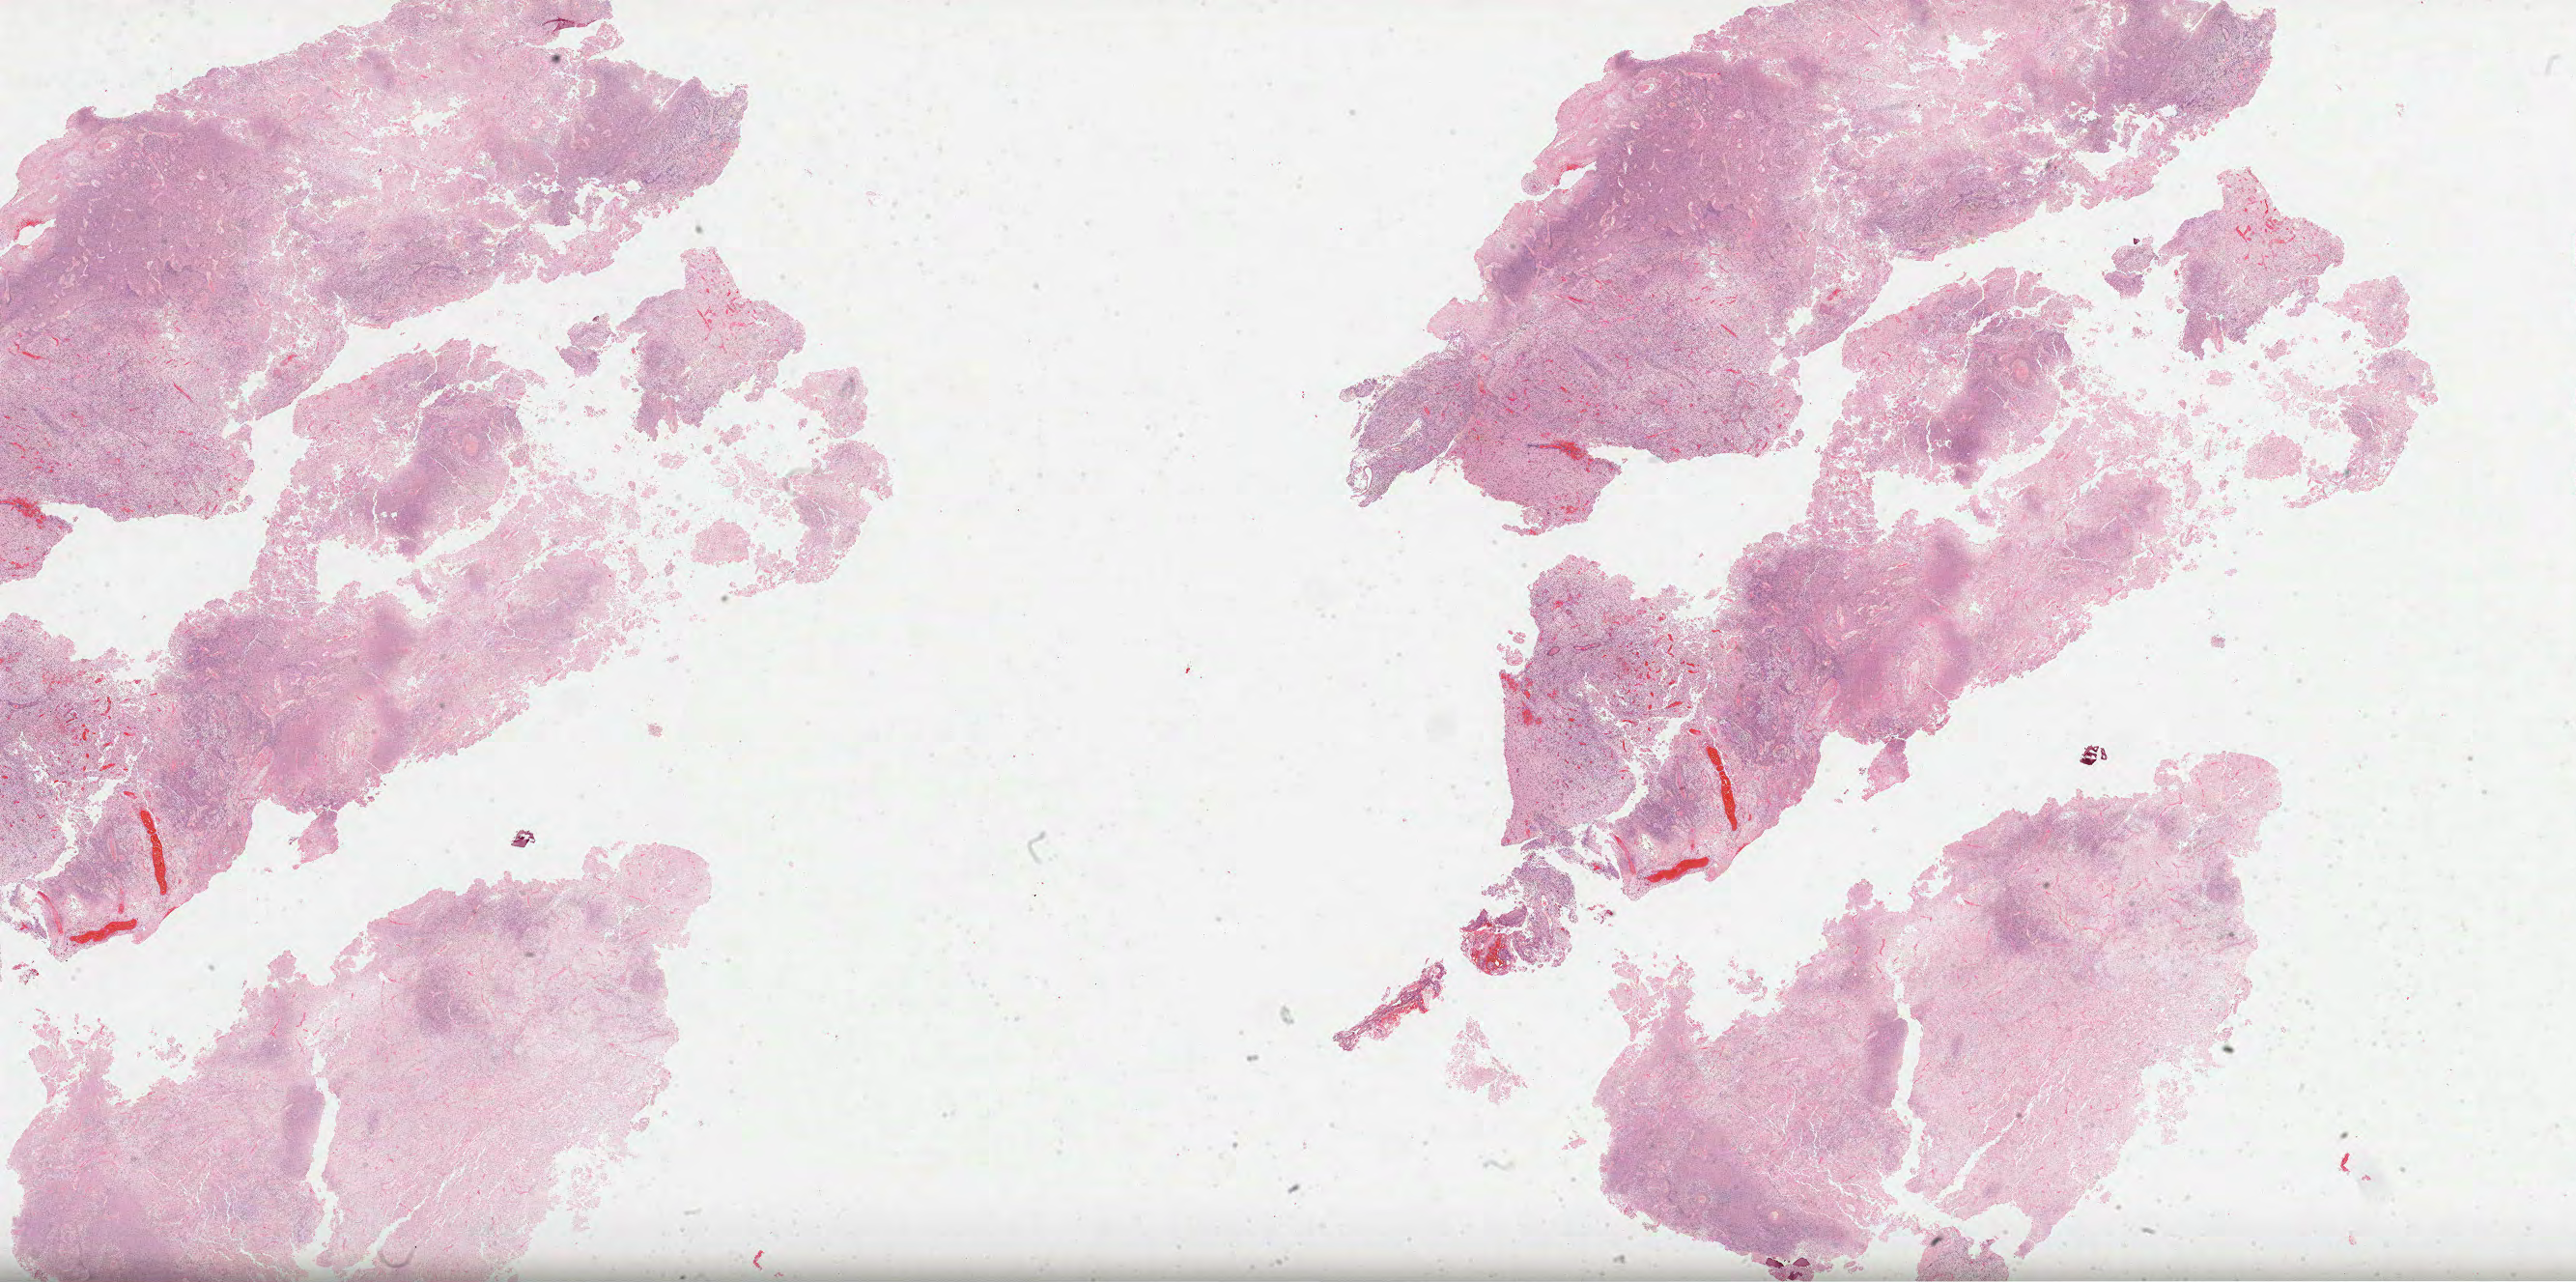
Whole-slide histology image, H&E, a low-resolution overview of the entire scanned area, about 43.0 x 21.4 mm (slide scanned at 40x); formalin-fixed paraffin-embedded (FFPE) diagnostic section; primary tumour sample from the brain. Patient: female, age at initial diagnosis 47 years.
Pathologic diagnosis: Glioblastoma.